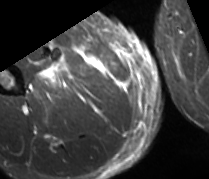
MRI of an extremity soft-tissue mass, one axial slice. Position 24 of 89 along the scan axis. STIR. MR volume resampled by the dataset authors to the PET/CT grid (not the native acquisition matrix). 209 × 179 image matrix, field of view 204 × 175 mm. Male patient. From the clinical record (not read from this slice): histological type: undifferentiated - pleiomorphic; grade: high; site of the primary tumour: right thigh.
Outlined on this slice (expert contour drawn on MRI and transferred to this co-registered scan by the dataset authors):
- gross tumour volume including surrounding oedema: box from (x=37, y=57) to (x=104, y=90) px